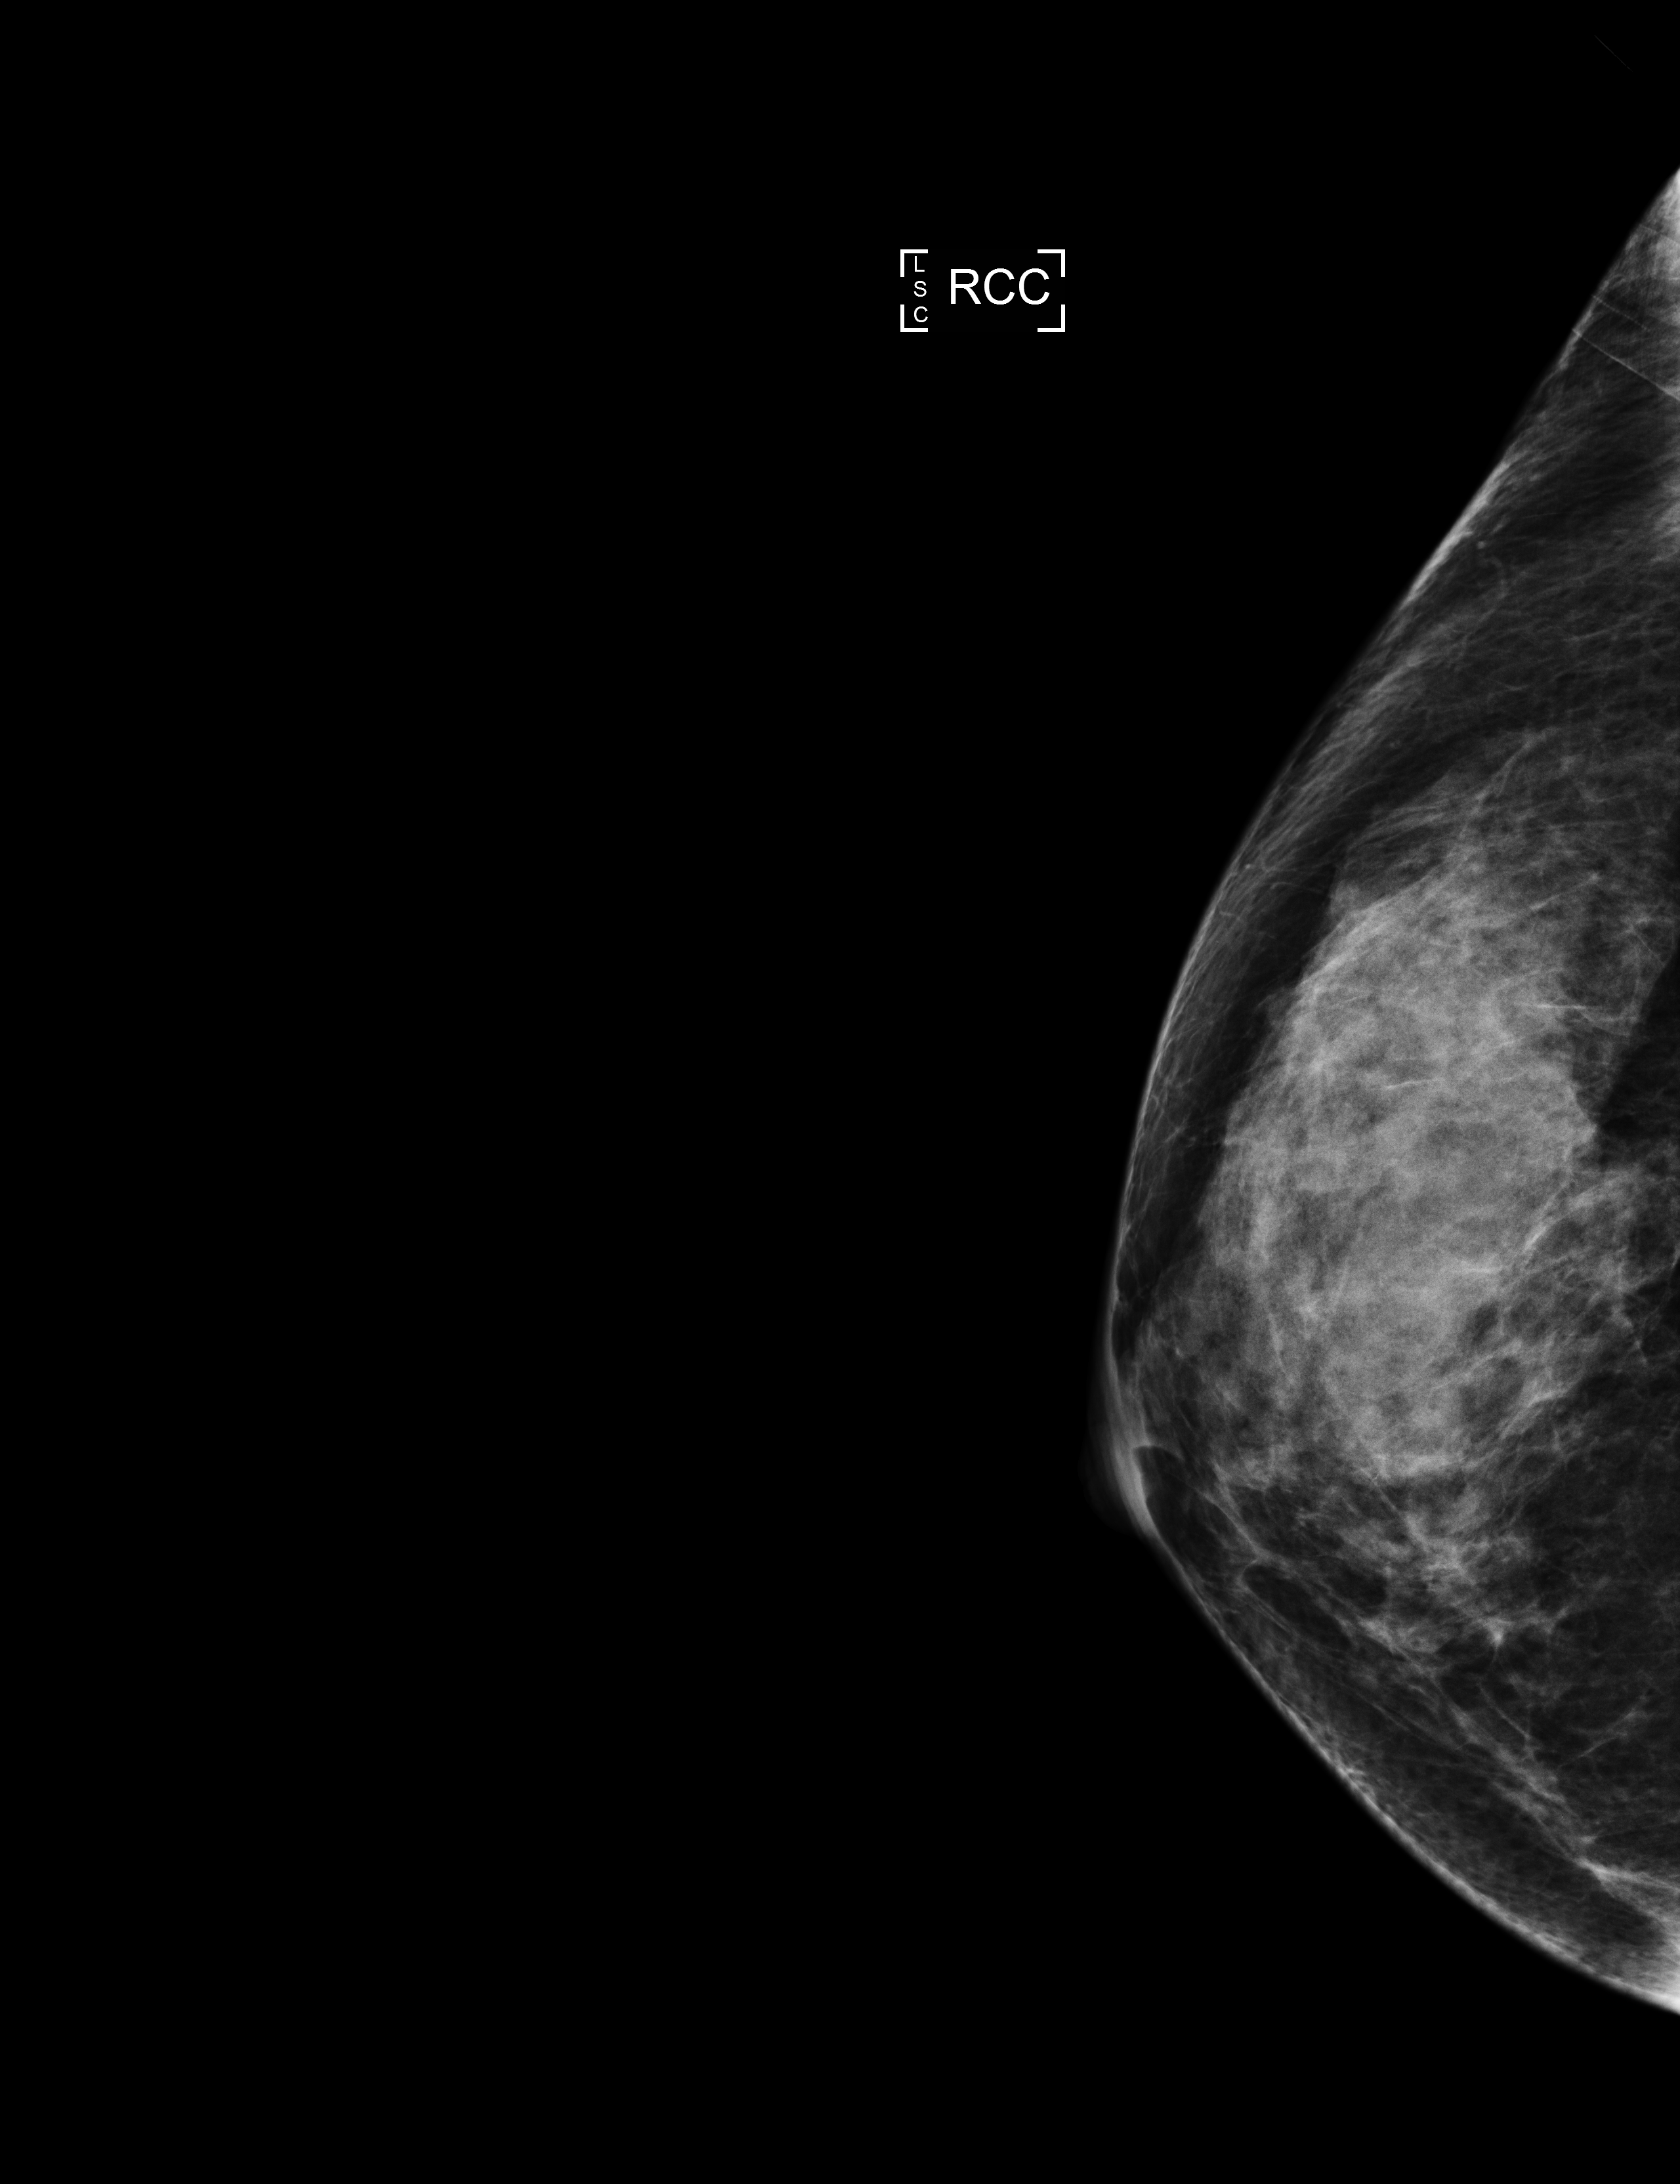
Annual screening mammography examination, system: Selenia Dimensions. Patient aged 51 years (female).
Image type: full-field digital mammogram. Breast: right. Projection: cranio-caudal projection.